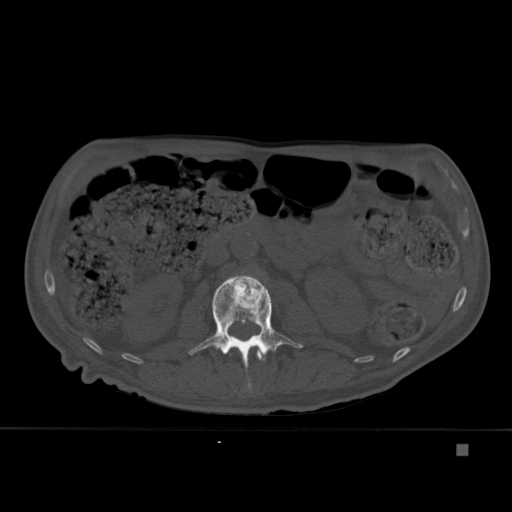
CT including the spine, one axial slice; slice 163 of 451 in the series (ordered by position); bone window (W 1800 / L 400 HU); 1.5 mm slice thickness; 512 × 512 image matrix, field of view 378 × 378 mm. Male patient, age 75 years. From the clinical record (not read from this slice): primary cancer: prostate.
Structures marked on this image (semi-automatically segmented with operator editing):
- L1 vertebra: box from (x=230, y=349) to (x=266, y=389) px
- L2 vertebra: (x=188, y=275)–(x=303, y=379)